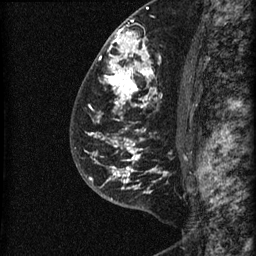
Breast MRI (dynamic contrast-enhanced), one sagittal slice. Slice 42 of 60 in the series (ordered by position). Dynamic contrast-enhanced series, image 2 of 3 at this slice position (ordered by acquisition). 1.5 T. TE 4.2 ms, TR 22.7 ms. 1.5 mm slice thickness. 256 × 256 image matrix, field of view 180 × 180 mm. Patient: female, 48 years. Case-level facts recorded for this patient, not image findings: setting: breast cancer imaged before/during neoadjuvant chemotherapy; receptor status: triple-negative.
Annotated regions visible in this slice (semi-automatically segmented with operator editing):
- analysis volume of interest (the breast-tissue region the enhancement analysis was run in; not a lesion): box from (x=81, y=23) to (x=186, y=202) px
- tumour enhancement mask (voxels above the 90 % enhancement threshold inside the analysis volume of interest): (x=89, y=29)–(x=166, y=192)